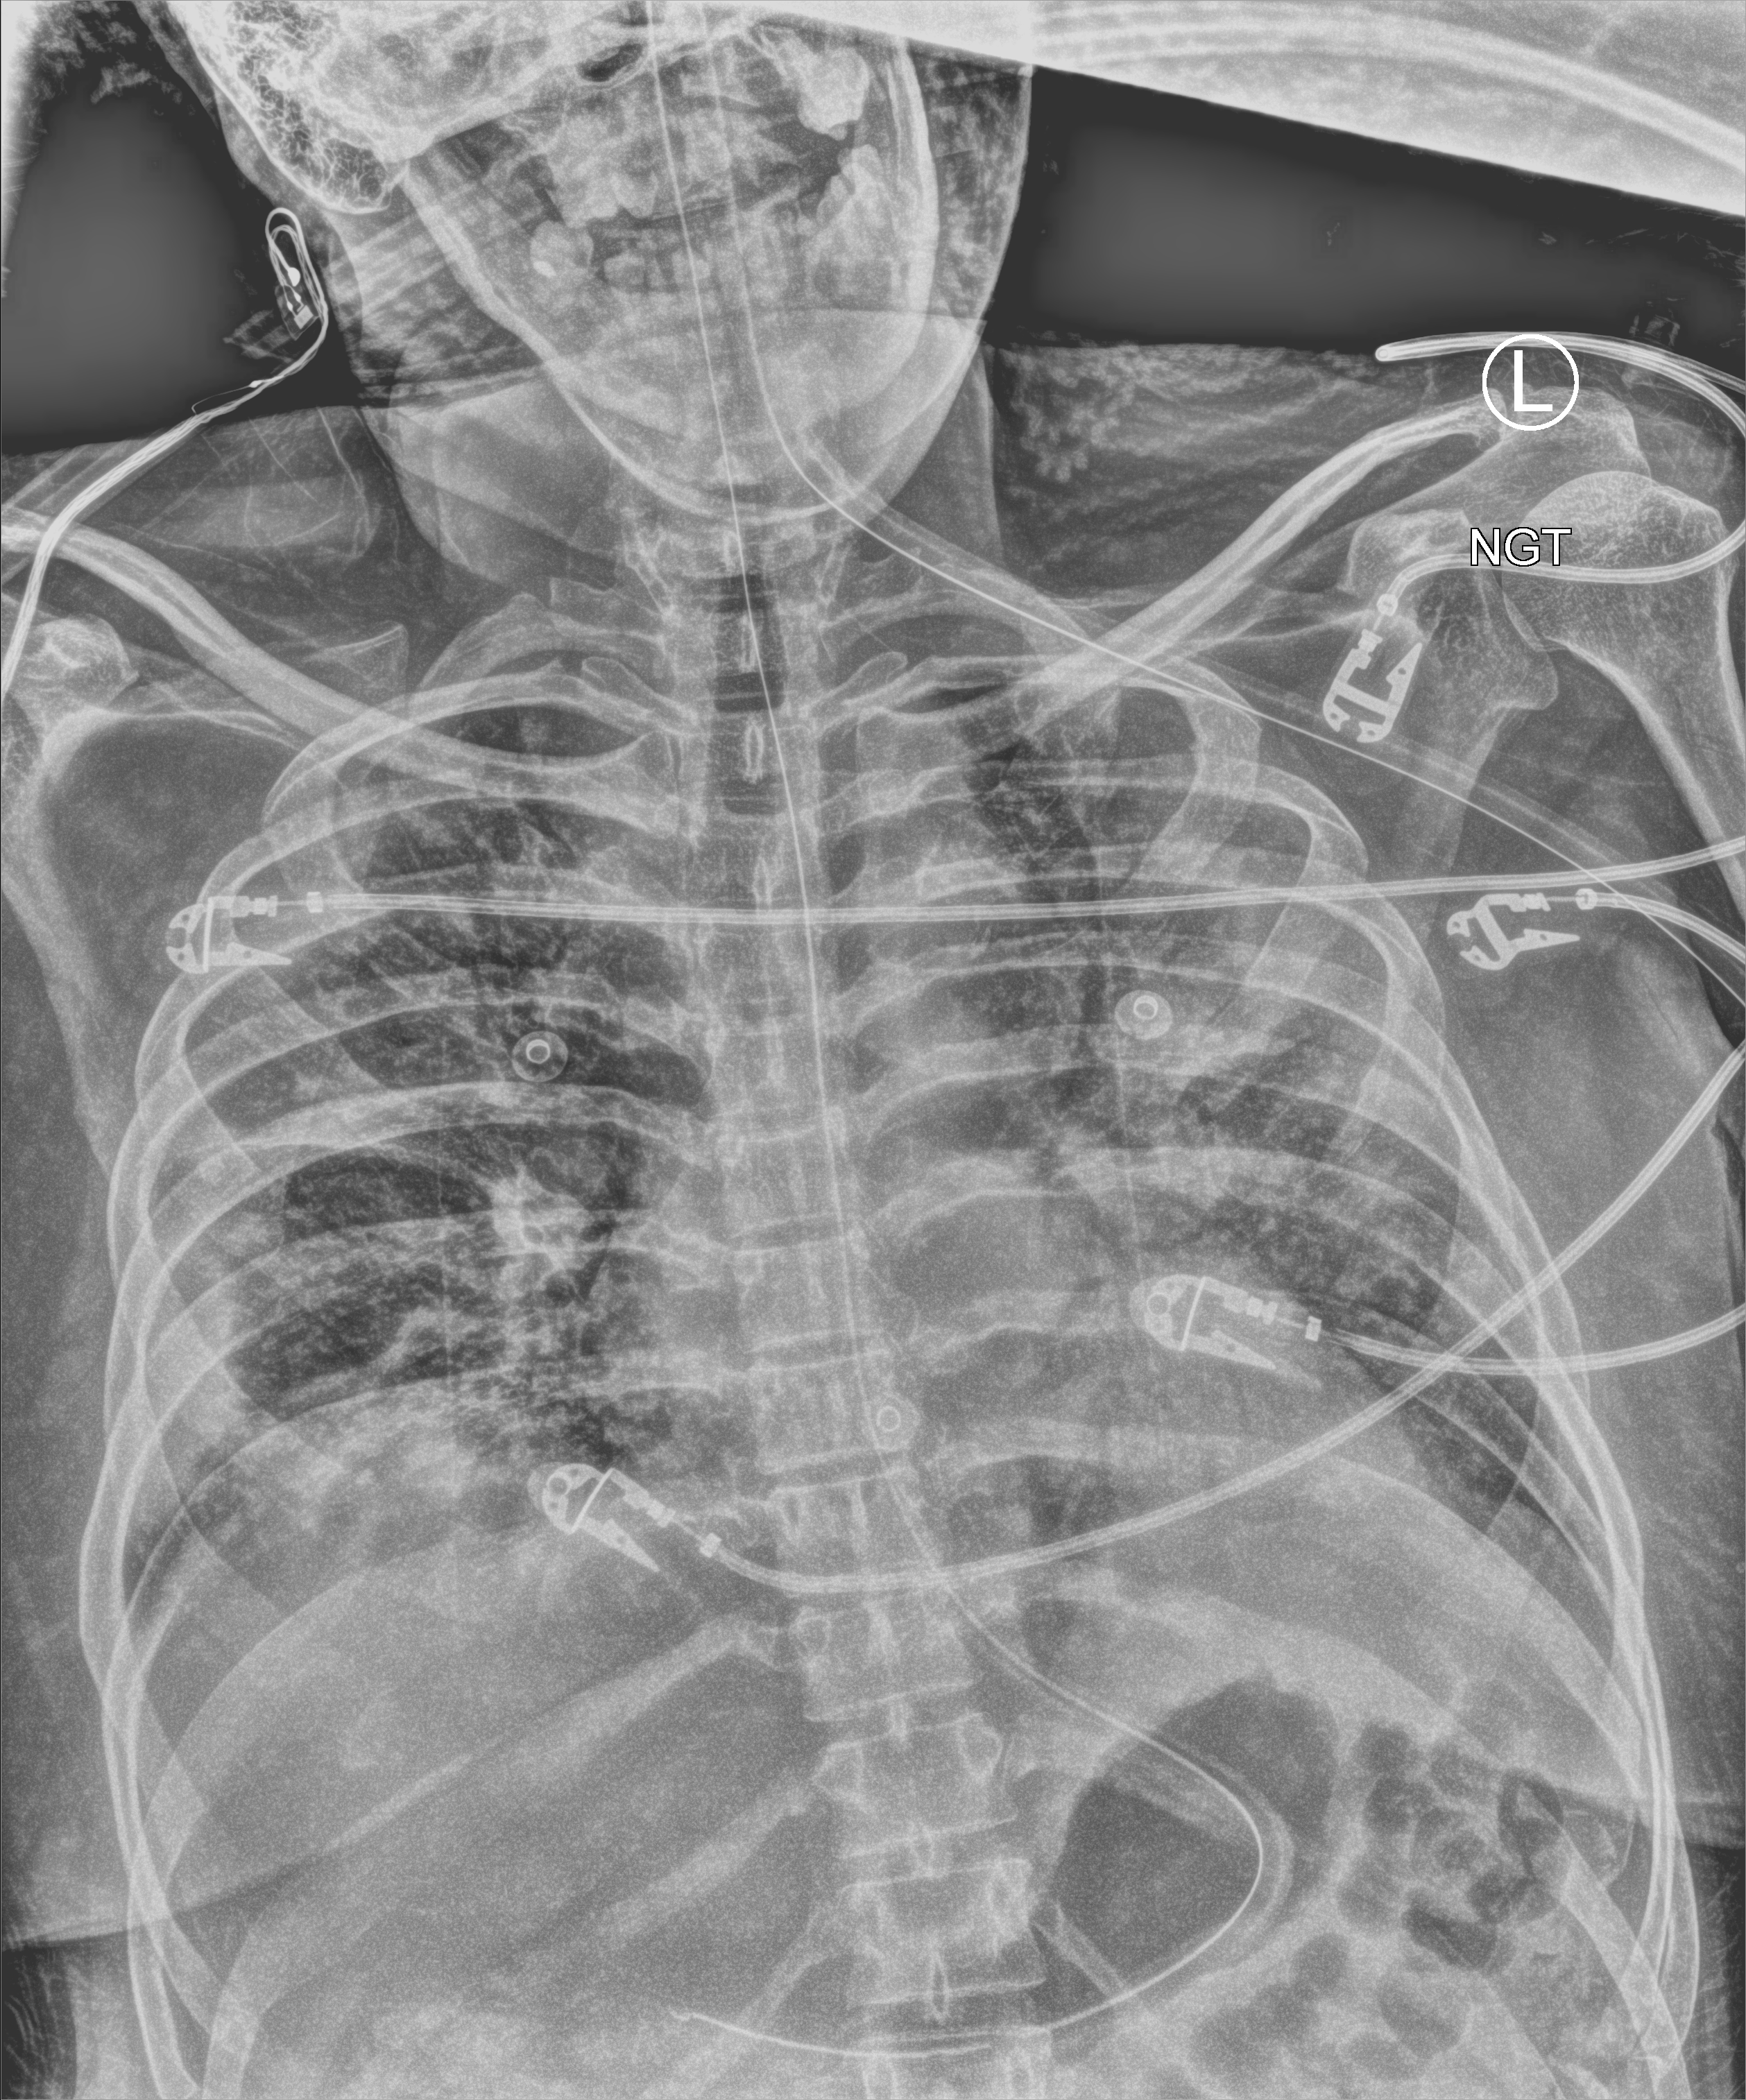
Portable chest radiograph, anteroposterior (AP) projection. Patient hospitalised with COVID-19, aged 18–59 years.
Hospital-stay facts (about this admission, not read from this image; timing relative to this image not recorded): COPD (admission record): no.